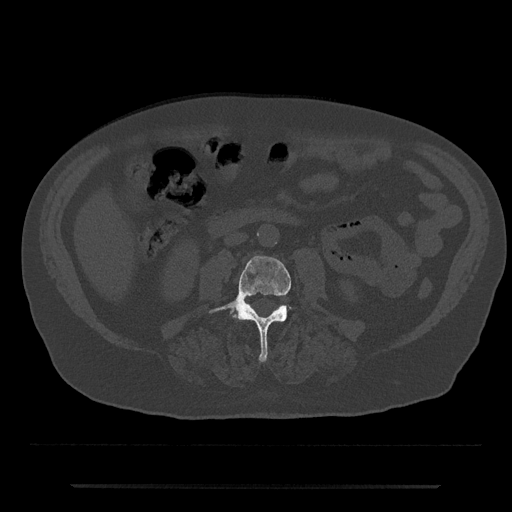
CT including the spine, one axial slice; slice 405 of 797 in the series (ordered by position); reconstruction kernel Br40s/3; bone window (W 1800 / L 400 HU); 0.5 mm slice thickness; 512 × 512 image matrix. Patient: male, 80 years. Case-level facts recorded for this patient, not image findings: primary cancer: prostate; vertebrae with lytic lesions (as recorded): L1, T11.
Annotated regions visible in this slice (semi-automatic segmentation, software-assisted and operator-edited):
- L3 vertebra: bounding box (x1, y1, x2, y2) in pixels: (209, 256, 291, 362)
- L4 vertebra: (233, 314, 237, 318)